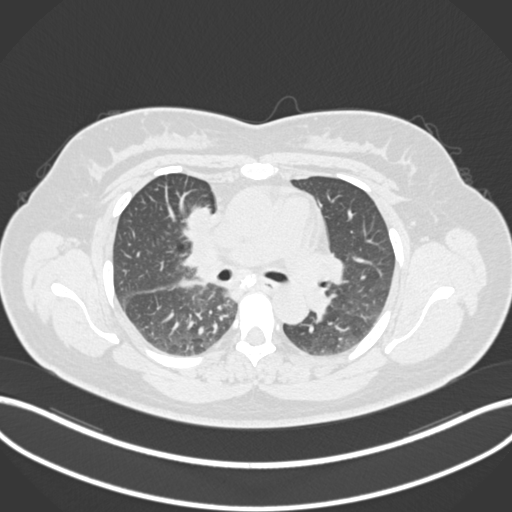
Chest CT, one axial slice. Slice 106 of 183 in the series (ordered by position). Reconstruction kernel B30f. Lung window (W 1500 / L -600 HU). 512 × 512 image matrix, field of view 400 × 400 mm. Female patient, age 46 years. Case-level facts recorded for this patient, not image findings: clinical TNM (as recorded): T2a N1 M0.
Outlined on this slice (bounding box drawn by a radiologist):
- lung tumour (recorded histology: adenocarcinoma): box from (x=183, y=201) to (x=212, y=232) px